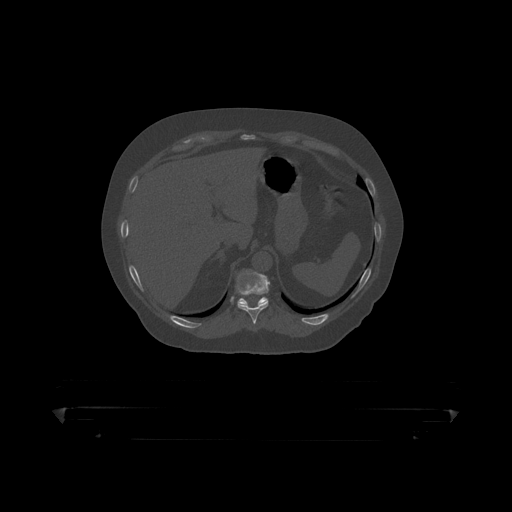
CT including the spine, one axial slice; position 209 of 390 along the scan axis; reconstruction kernel STANDARD; bone window (W 1800 / L 400 HU); 1.25 mm slice thickness; 512 × 512 image matrix, field of view 650 × 650 mm. Patient: male, 60 years. Case-level facts recorded for this patient, not image findings: primary cancer: prostate.
Structures marked on this image (semi-automatic segmentation, software-assisted and operator-edited):
- T10 vertebra: bounding box <236,270,271,319> (left, top, right, bottom; pixels)
- T11 vertebra: <231,298,268,306>